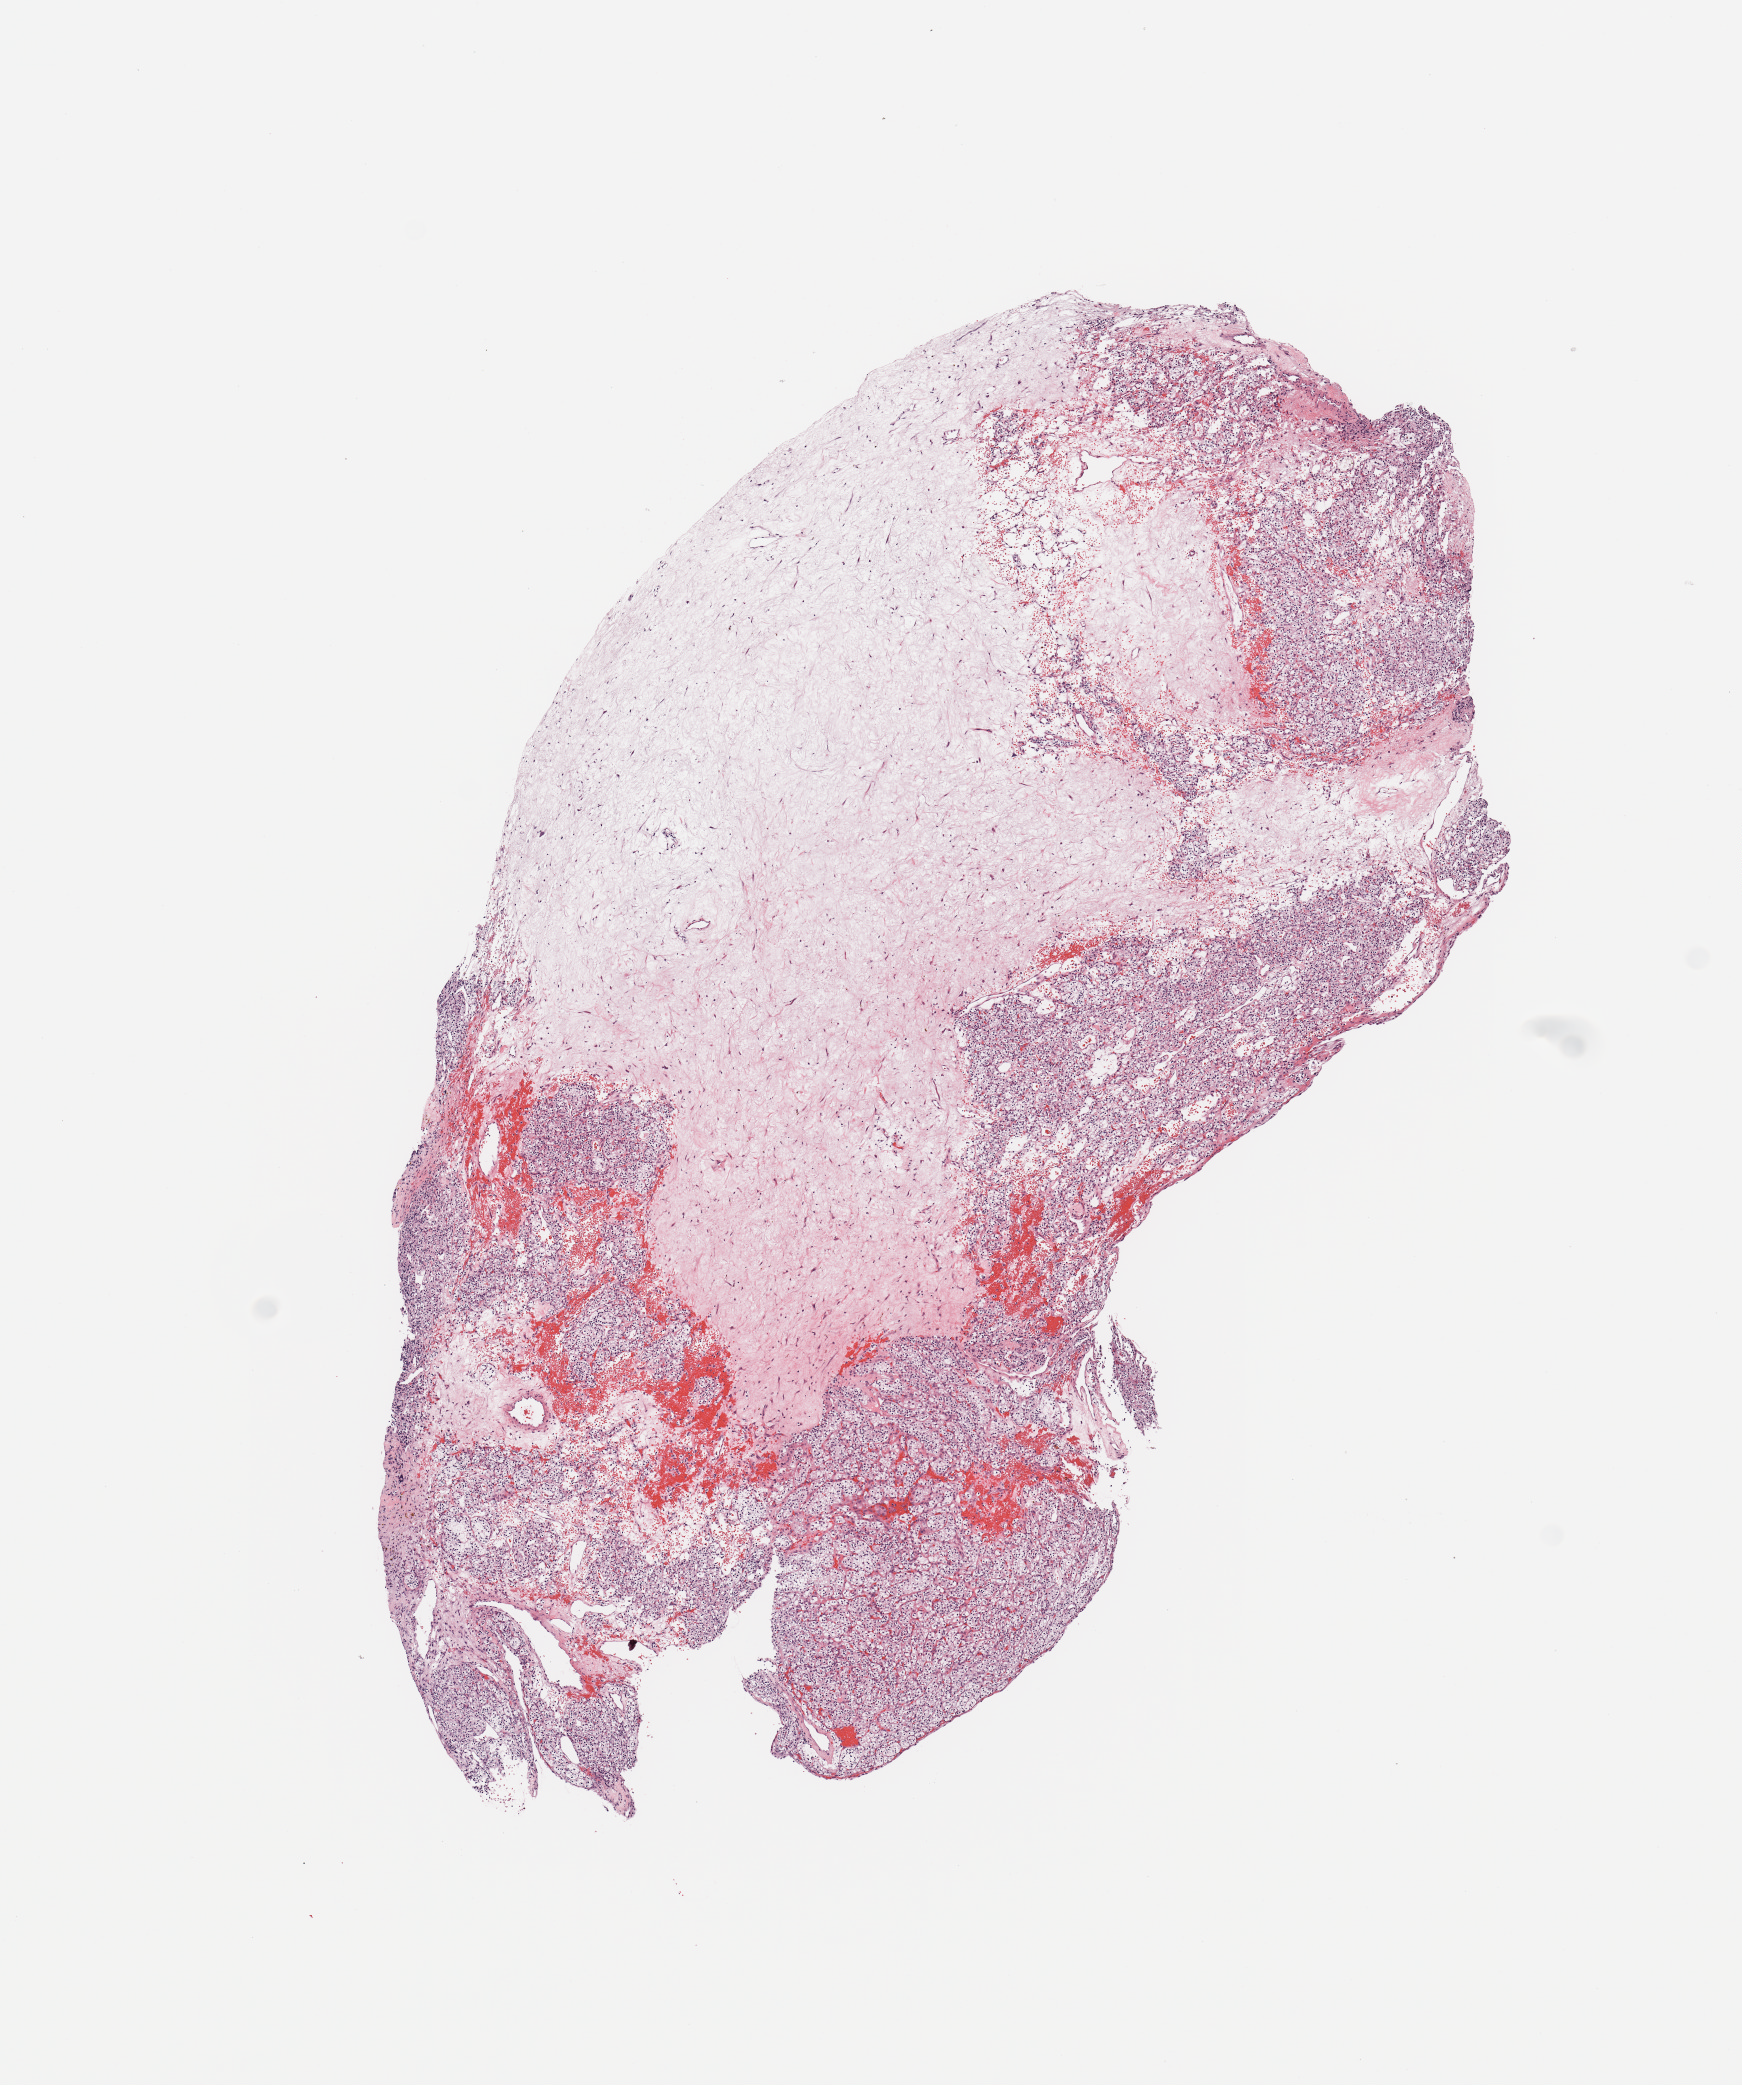
Whole-slide histology image, Hematoxylin and eosin (H&E) stained, whole scanned area (about 6.9 x 8.2 mm) shown as a low-resolution overview. Tumour tissue sample, sampled site: kidney. 51-year-old male patient. Histologic grade: G2 (moderately differentiated). Pathologist review of this section (percent, as recorded): tumour nuclei 80%, necrosis 5%.
AJCC pathologic stage: I. Diagnosis: Renal cell carcinoma, NOS. Primary tumour site (as recorded): lower pole.